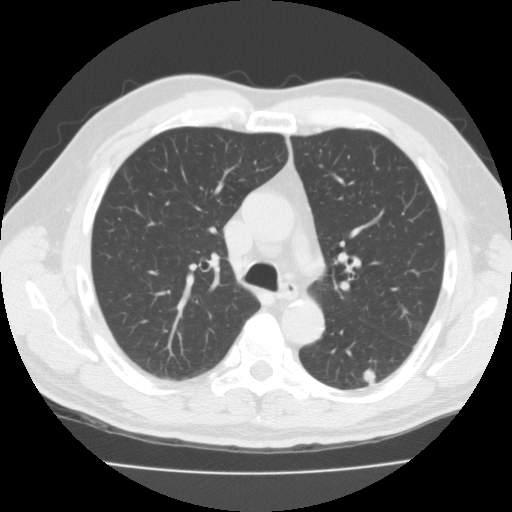
Low-dose screening chest CT, one axial slice; position 67 of 99 along the scan axis; 120 kVp; lung window (W 1500 / L -600 HU); 3 mm slice thickness; 512 × 512 image matrix, field of view 359 × 359 mm.
Annotated regions visible in this slice (outlined manually by an expert reader):
- lesion 1 (tumor, lower lobe of left lung): bounding box [x1, y1, x2, y2] px = [363, 368, 376, 387]